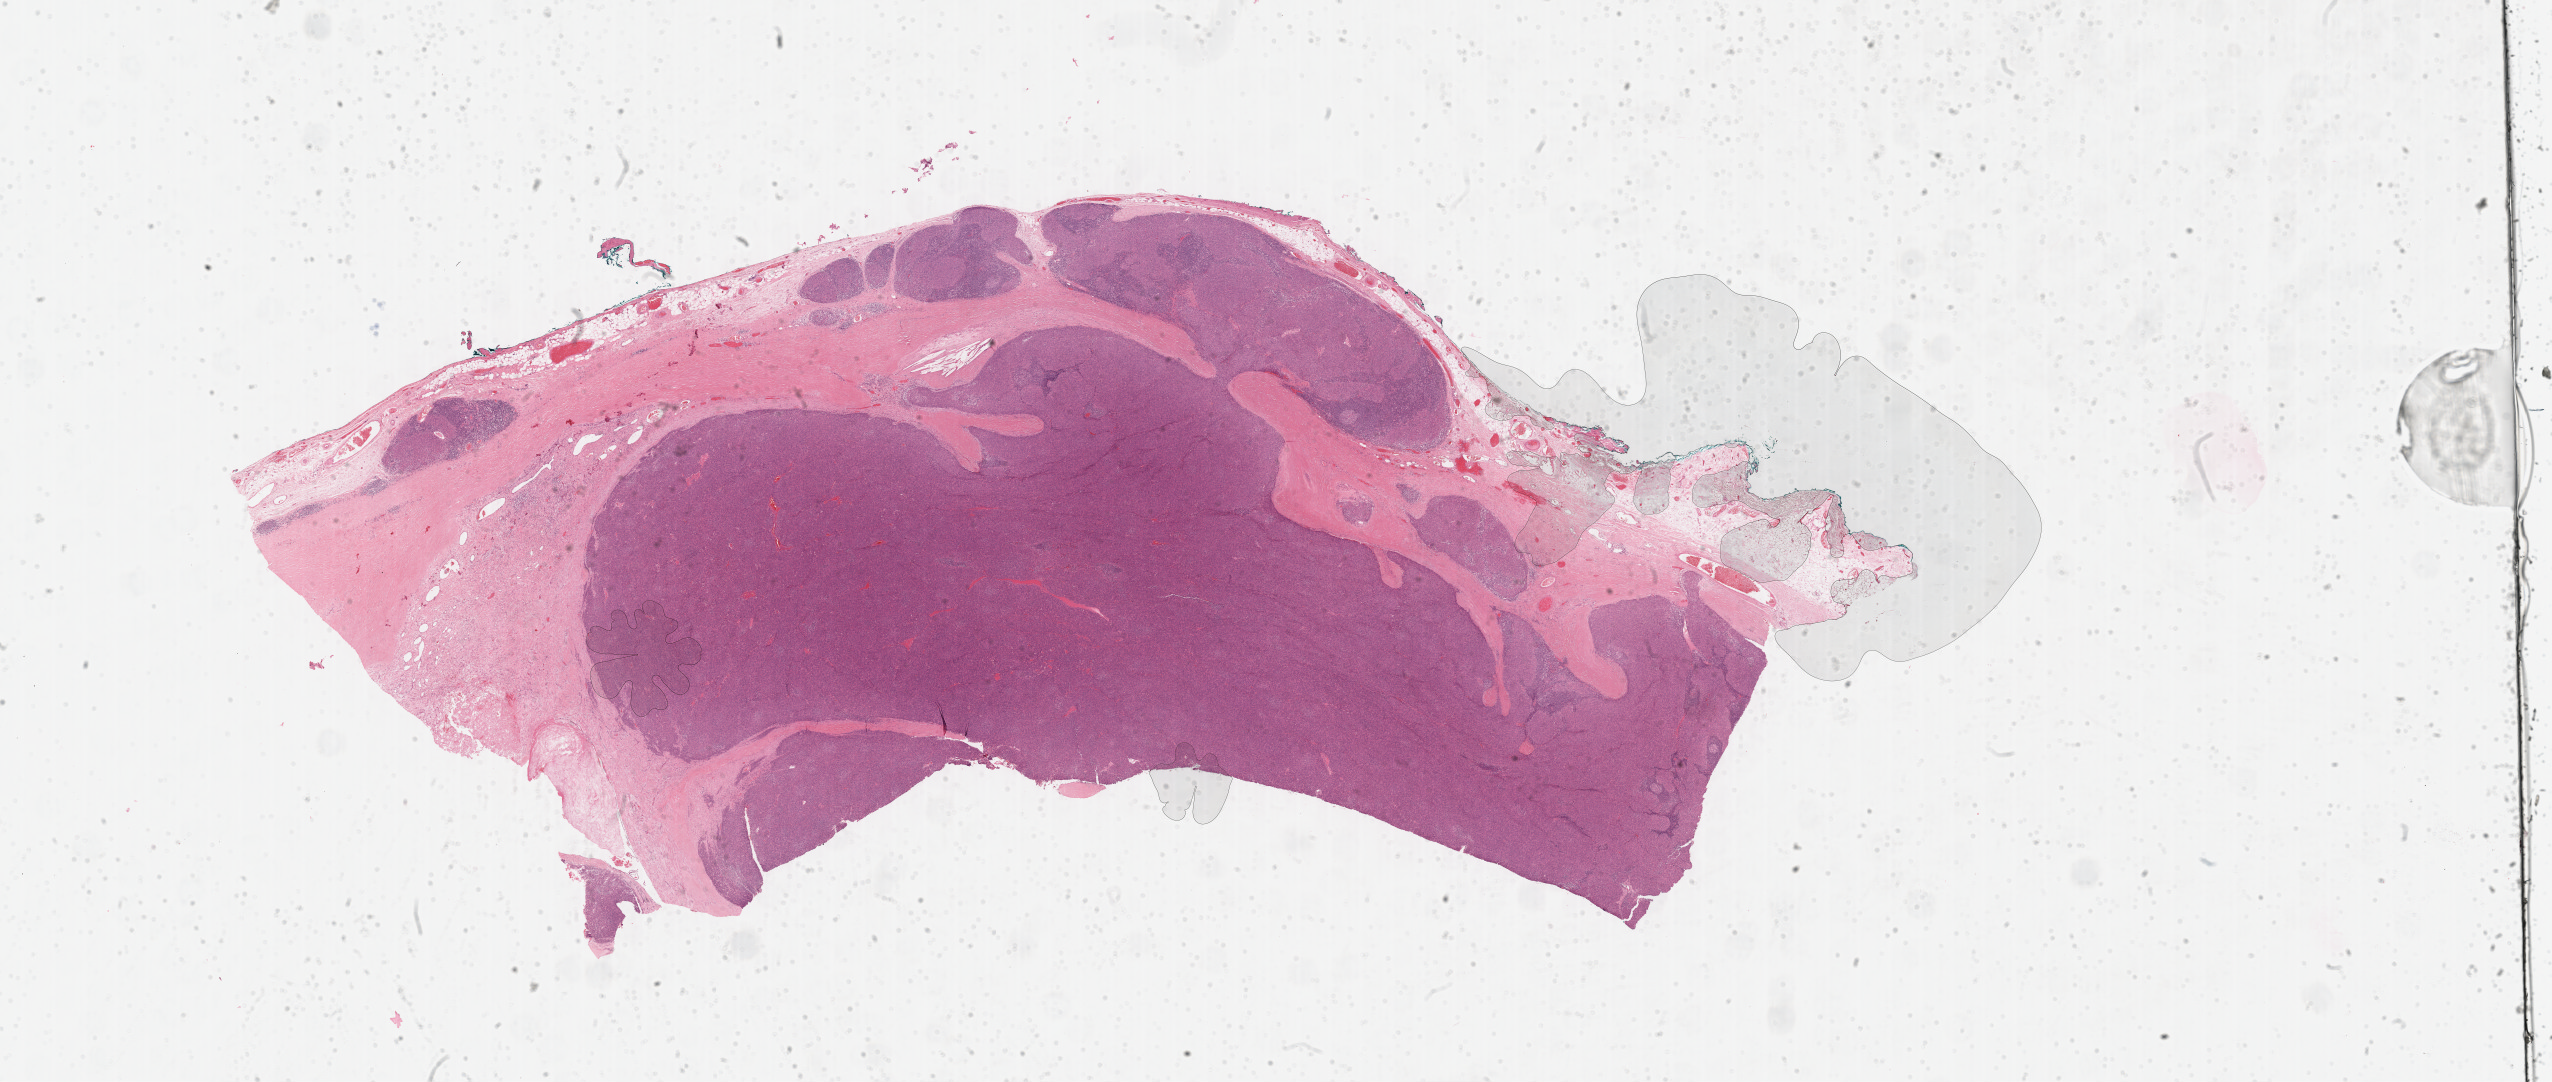
Whole-slide histology image, H&E, whole scanned area (about 41.3 x 17.5 mm, acquisition: 40x scan) shown as a low-resolution overview. FFPE section. Sample: primary tumour, thymus. Patient: female, age at initial diagnosis 64 years.
- diagnosis: Thymoma, type B3, malignant